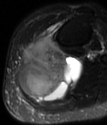
MRI of an extremity soft-tissue mass, one axial slice; slice 38 of 78 in the series (ordered by position); T2-weighted fat-saturated; MR volume resampled by the dataset authors to the PET/CT grid (not the native acquisition matrix); 107 × 125 image matrix, field of view 104 × 122 mm. Female patient. From the clinical record (not read from this slice): histological type: extraskeletal high grade osteogenic sarcoma; grade: high; site of the primary tumour: left calf.
Annotated regions visible in this slice (expert contour drawn on MRI and transferred to this co-registered scan by the dataset authors):
- gross tumour volume (mass): bounding box <19,36,81,103> (left, top, right, bottom; pixels)